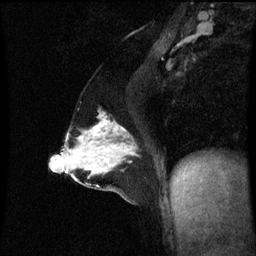
Breast MRI (dynamic contrast-enhanced), one sagittal slice; position 34 of 60 along the scan axis; dynamic contrast-enhanced series, image 2 of 3 at this slice position (ordered by acquisition); 1.5 T; TE 4.2 ms, TR 8.9 ms; 2.1 mm slice thickness; 256 × 256 image matrix, field of view 200 × 200 mm. Patient: female, 47 years. From the clinical record (not read from this slice): setting: breast cancer imaged before/during neoadjuvant chemotherapy; receptor status: HR-positive, HER2-negative.
Annotated regions visible in this slice (semi-automatic segmentation, software-assisted and operator-edited):
- analysis volume of interest (the breast-tissue region the enhancement analysis was run in; not a lesion): box from (x=71, y=116) to (x=140, y=163) px
- tumour enhancement mask (voxels above the 70 % enhancement threshold inside the analysis volume of interest): (x=94, y=116)–(x=133, y=155)